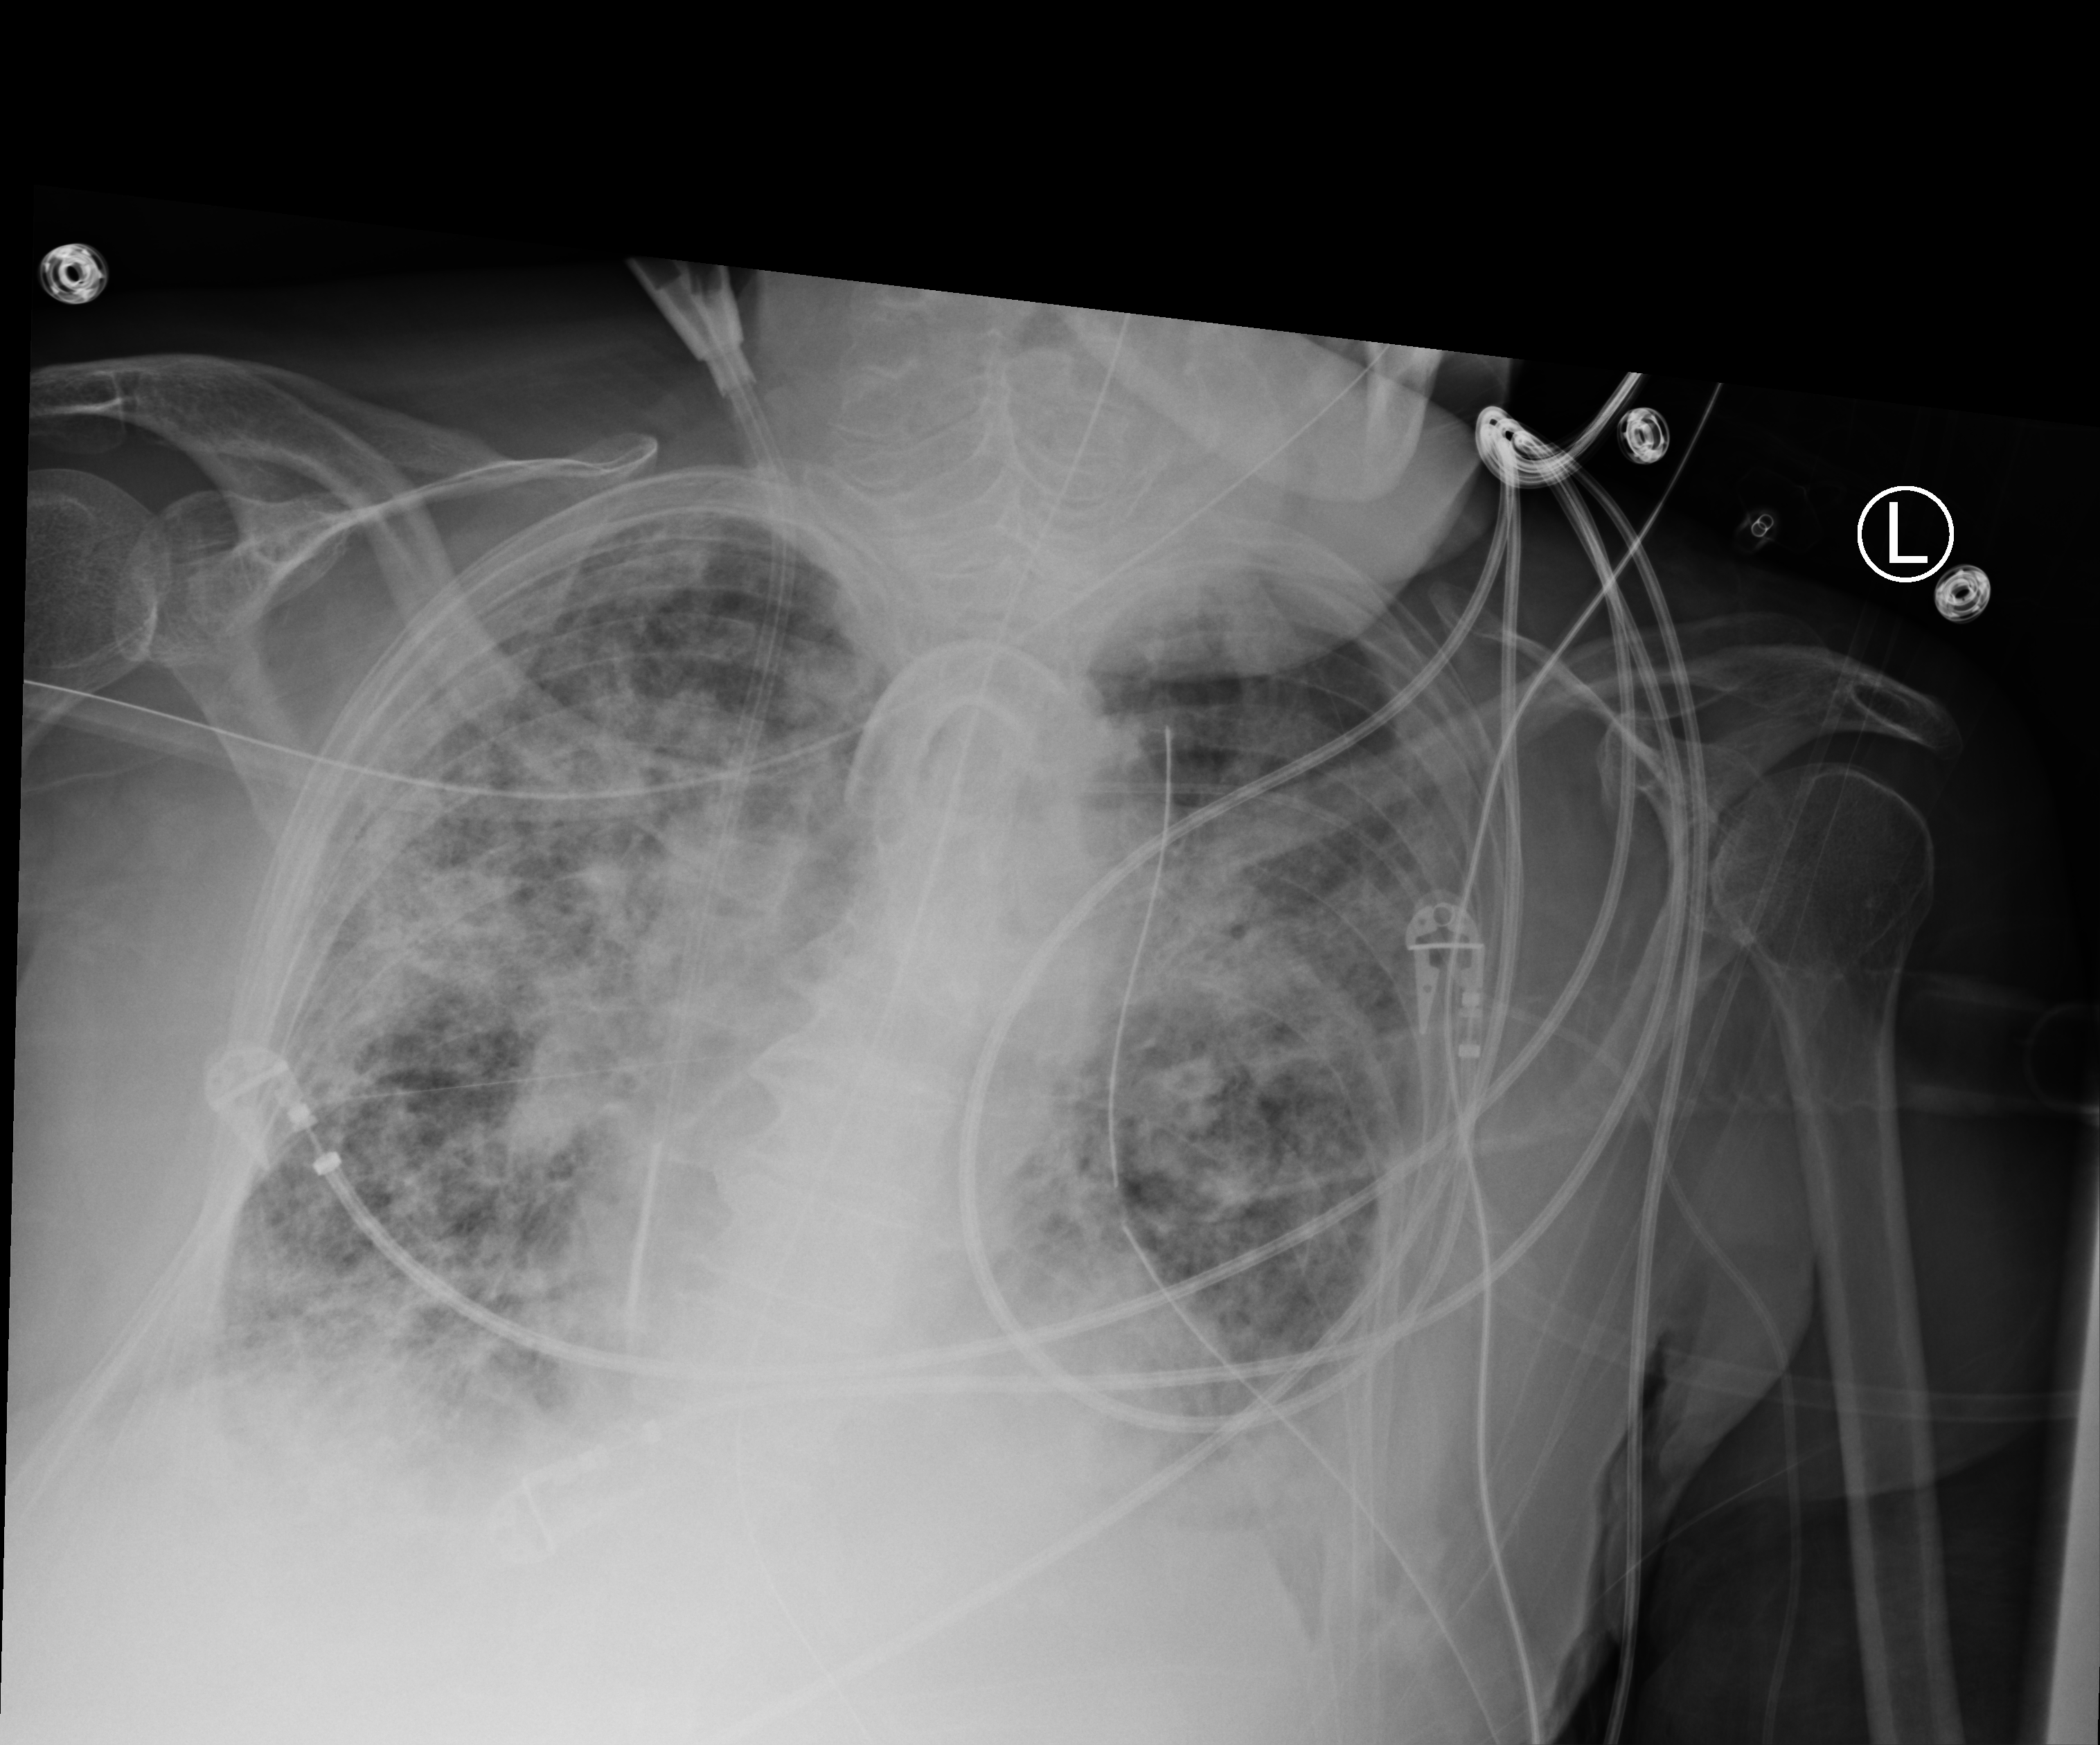
Portable chest radiograph; anteroposterior (AP) projection. Patient hospitalised with COVID-19; female, aged 75–90 years.
From the hospital-stay record, not from the radiograph (when in the stay this image was taken is not recorded): admitted to intensive care during this hospital stay: yes.